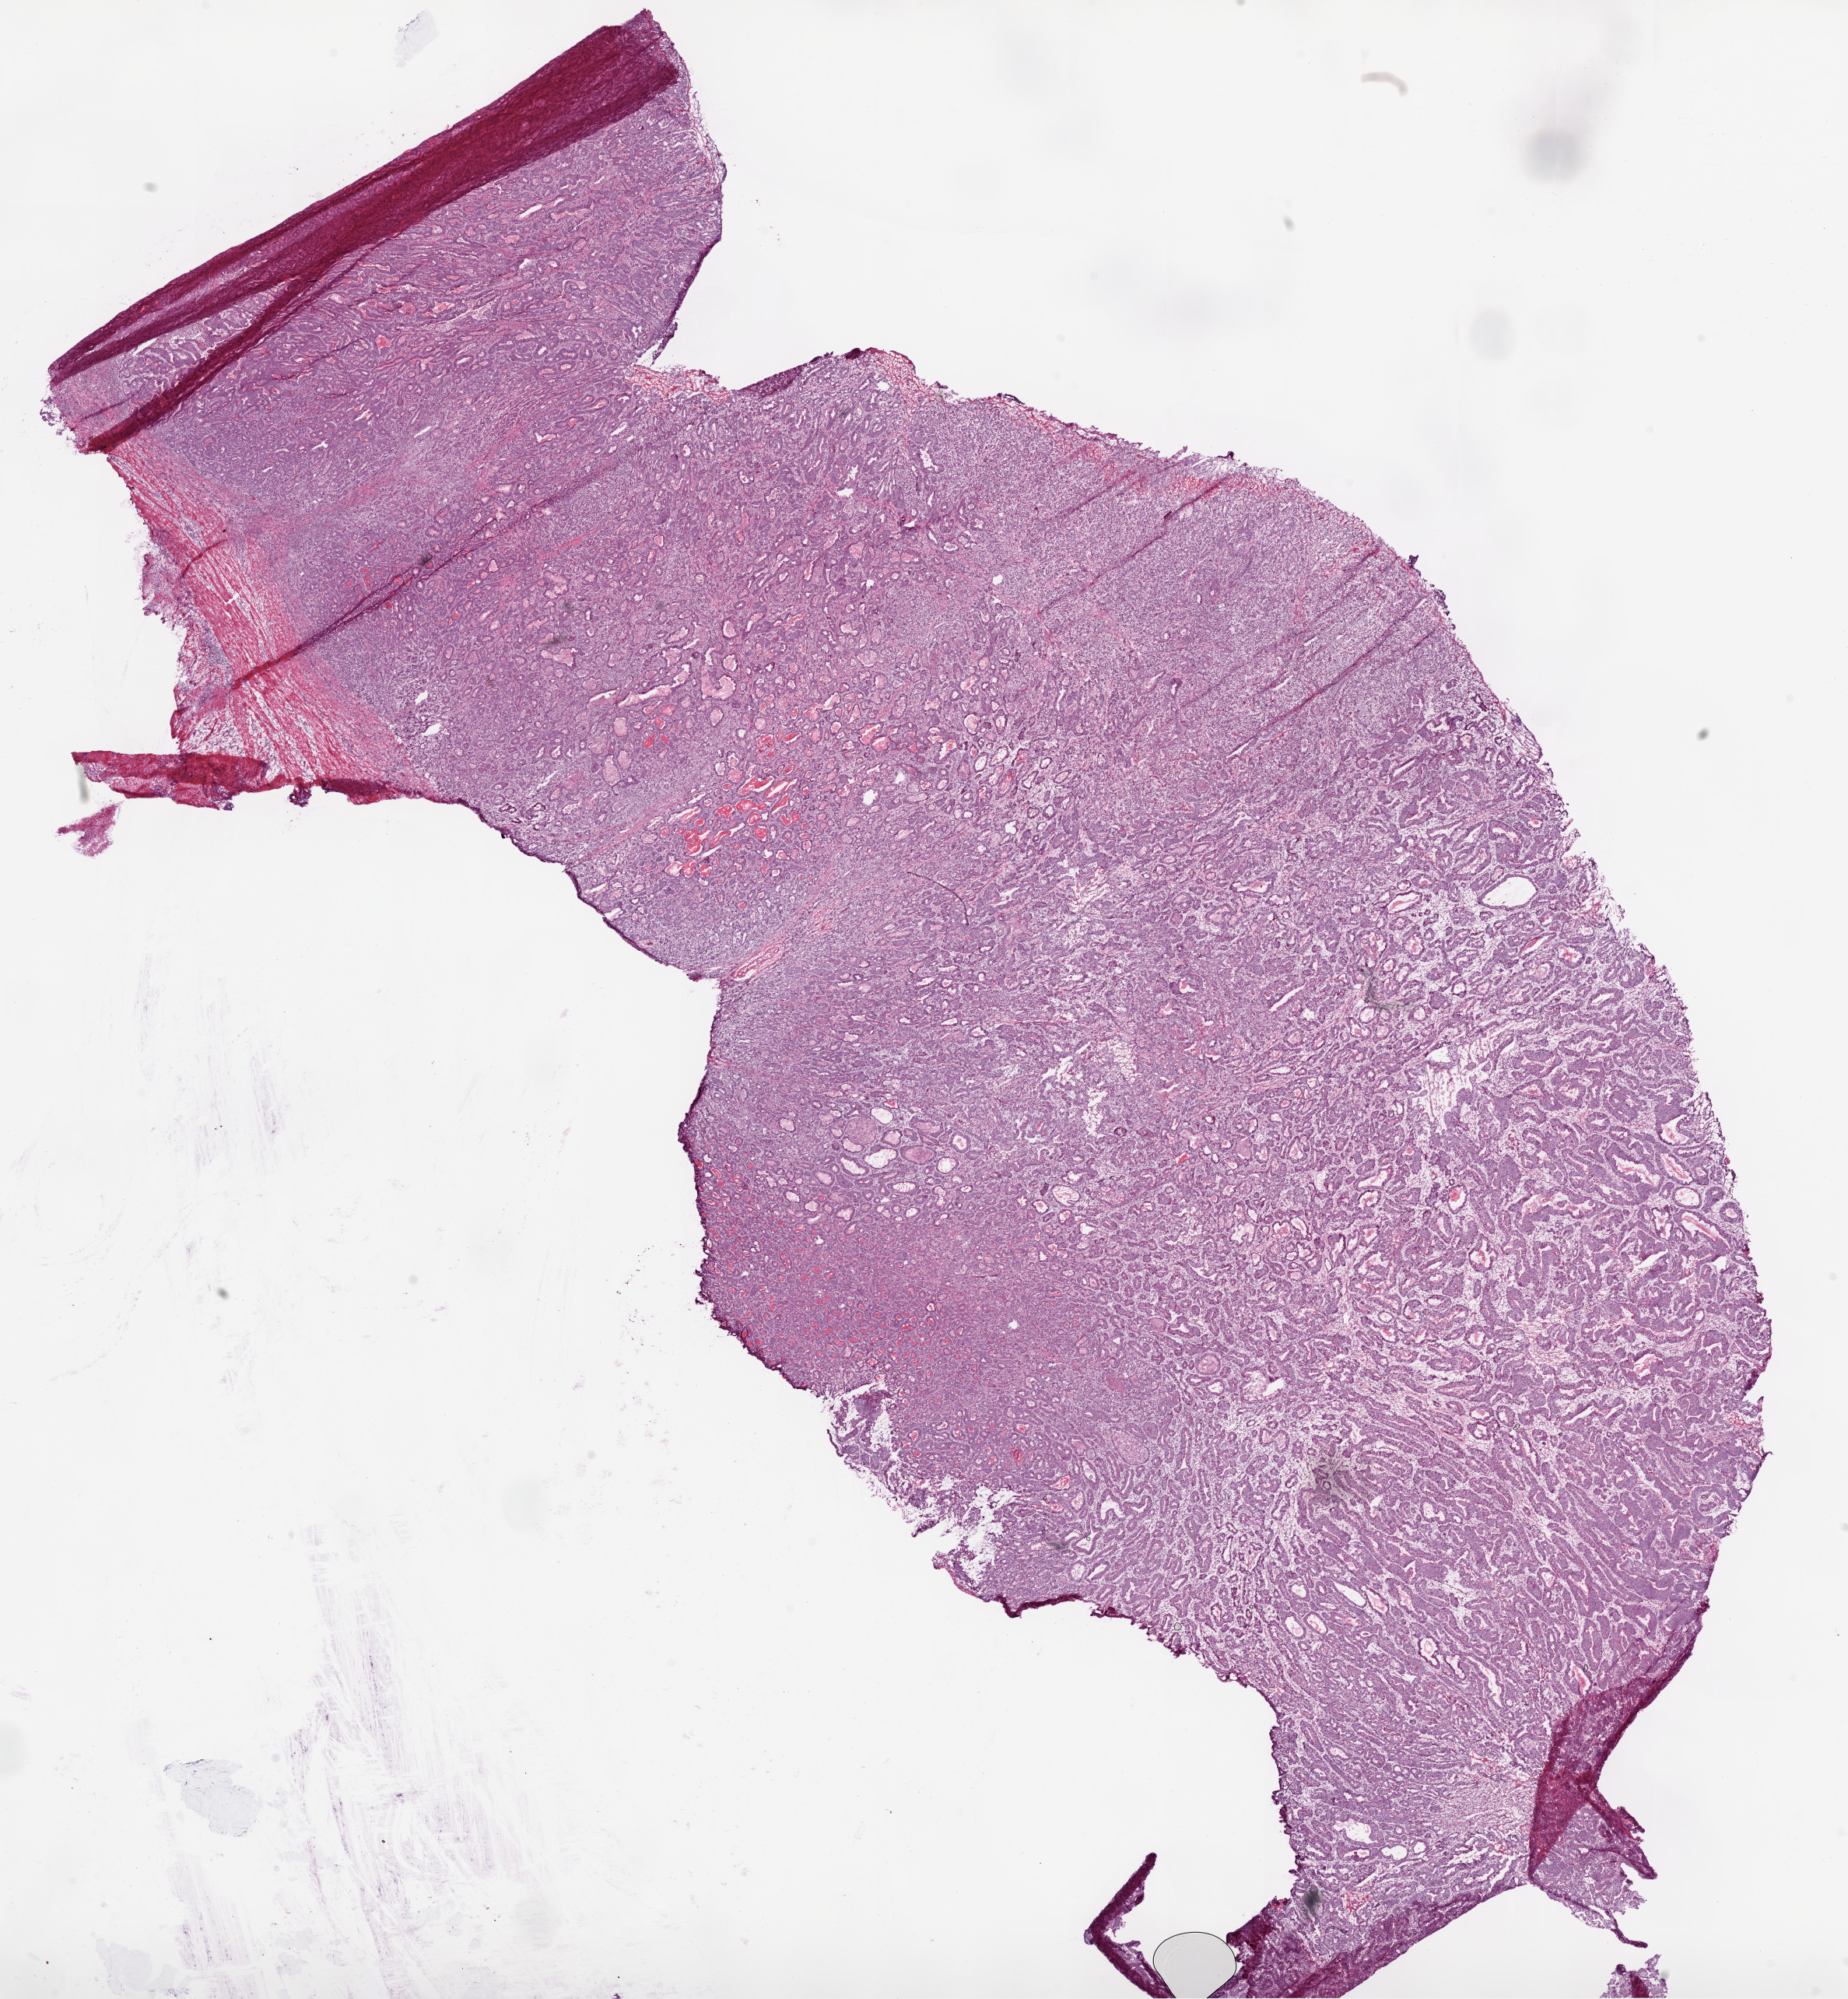
Hematoxylin and eosin (H&E) stained whole-slide image — a low-resolution overview of the entire scanned area, about 19.1 x 20.6 mm, frozen section, sample: primary tumour, stomach. Patient: female, age at initial diagnosis 78 years. Histologic grade: G2 (moderately differentiated). Pathologist review of this section (percent, as recorded): tumour cells 80%, tumour nuclei 85%, normal cells 0%, stromal cells 5%, necrosis 15%.
AJCC pathologic stage: III (6th edition). Pathologic diagnosis: Adenocarcinoma, NOS. TNM: T2b N1 M0. Lymph nodes positive (case pathology): 1 of 6 examined.